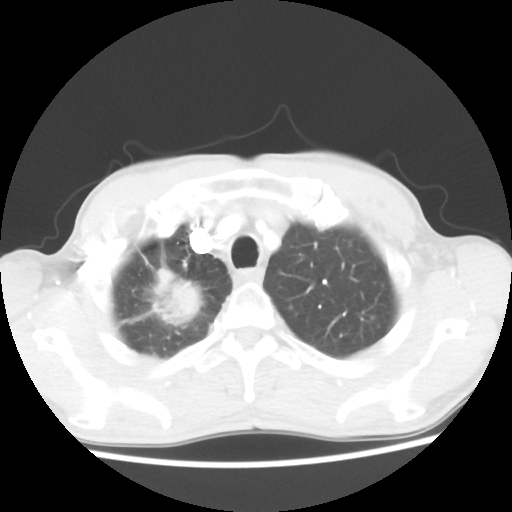
Chest CT, one axial slice. Position 45 of 52 along the scan axis. Lung window (W 1500 / L -600 HU). 5 mm slice thickness. 512 × 512 image matrix, field of view 323 × 323 mm. Patient: male, 66 years. Case-level facts recorded for this patient, not image findings: clinical TNM (as recorded): T2 N0 M1a.
Annotated regions visible in this slice (bounding box drawn by a radiologist):
- lung tumour (recorded histology: adenocarcinoma): box from (x=128, y=259) to (x=209, y=332) px